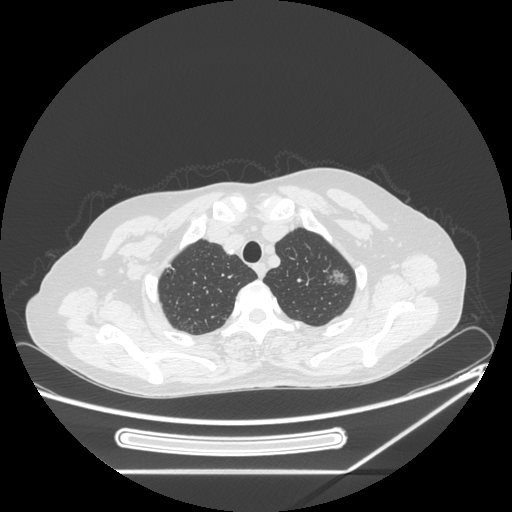
Chest CT, one axial slice. Position 207 of 250 along the scan axis. Reconstruction kernel STANDARD. 120 kVp. Lung window (W 1500 / L -600 HU). 1.25 mm slice thickness. 512 × 512 image matrix, field of view 409 × 409 mm. Patient: female, 57 years. From the clinical record (not read from this slice): clinical TNM (as recorded): T1c N0 M0.
Annotated regions visible in this slice (rectangle marked by the reading radiologist):
- lung tumour (recorded histology: adenocarcinoma): bounding box <320,262,355,290> (left, top, right, bottom; pixels)